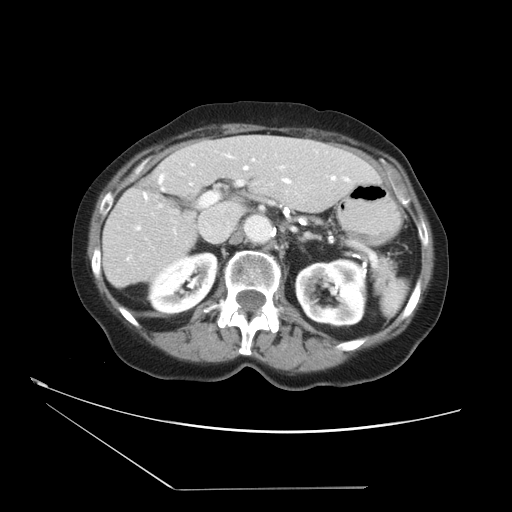
Contrast-enhanced abdominal CT, one axial slice. 120 kVp. Intravenous contrast given. Soft-tissue window (W 400 / L 40 HU). 5 mm slice thickness. 512 × 512 image matrix, field of view 384 × 384 mm. Female patient, age 81 years. Case-level facts recorded for this patient, not image findings: diagnosis: colorectal cancer liver metastases, imaged before liver resection; multiple liver metastases: no; largest metastasis: 1.6 cm; disease in both lobes: no.
Structures marked on this image (manually delineated by an expert):
- hepatic veins: bounding box (x1, y1, x2, y2) in pixels: (135, 167, 335, 243)
- liver: (103, 137, 382, 287)
- planned liver remnant (the part of the liver to remain after resection): (103, 139, 382, 287)
- portal vein (with intrahepatic branches): (144, 182, 243, 207)